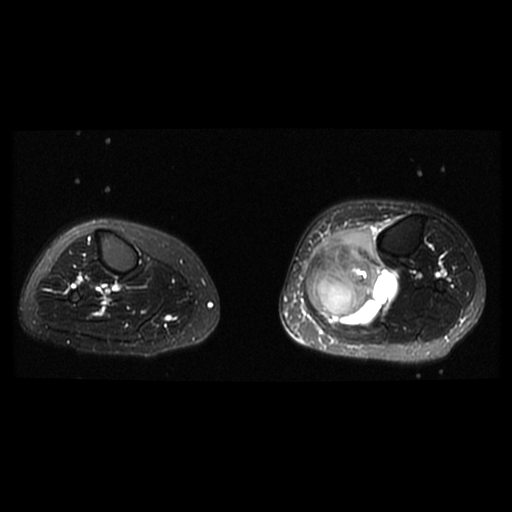
MRI of an extremity soft-tissue mass, one axial slice; T2-weighted fat-saturated; 512 × 512 image matrix, field of view 330 × 330 mm. Female patient. Case-level facts recorded for this patient, not image findings: histological type: extraskeletal high grade osteogenic sarcoma; grade: high; site of the primary tumour: left calf.
Structures marked on this image (manually delineated by an expert):
- gross tumour volume (mass): bounding box [x1, y1, x2, y2] px = [308, 228, 399, 325]